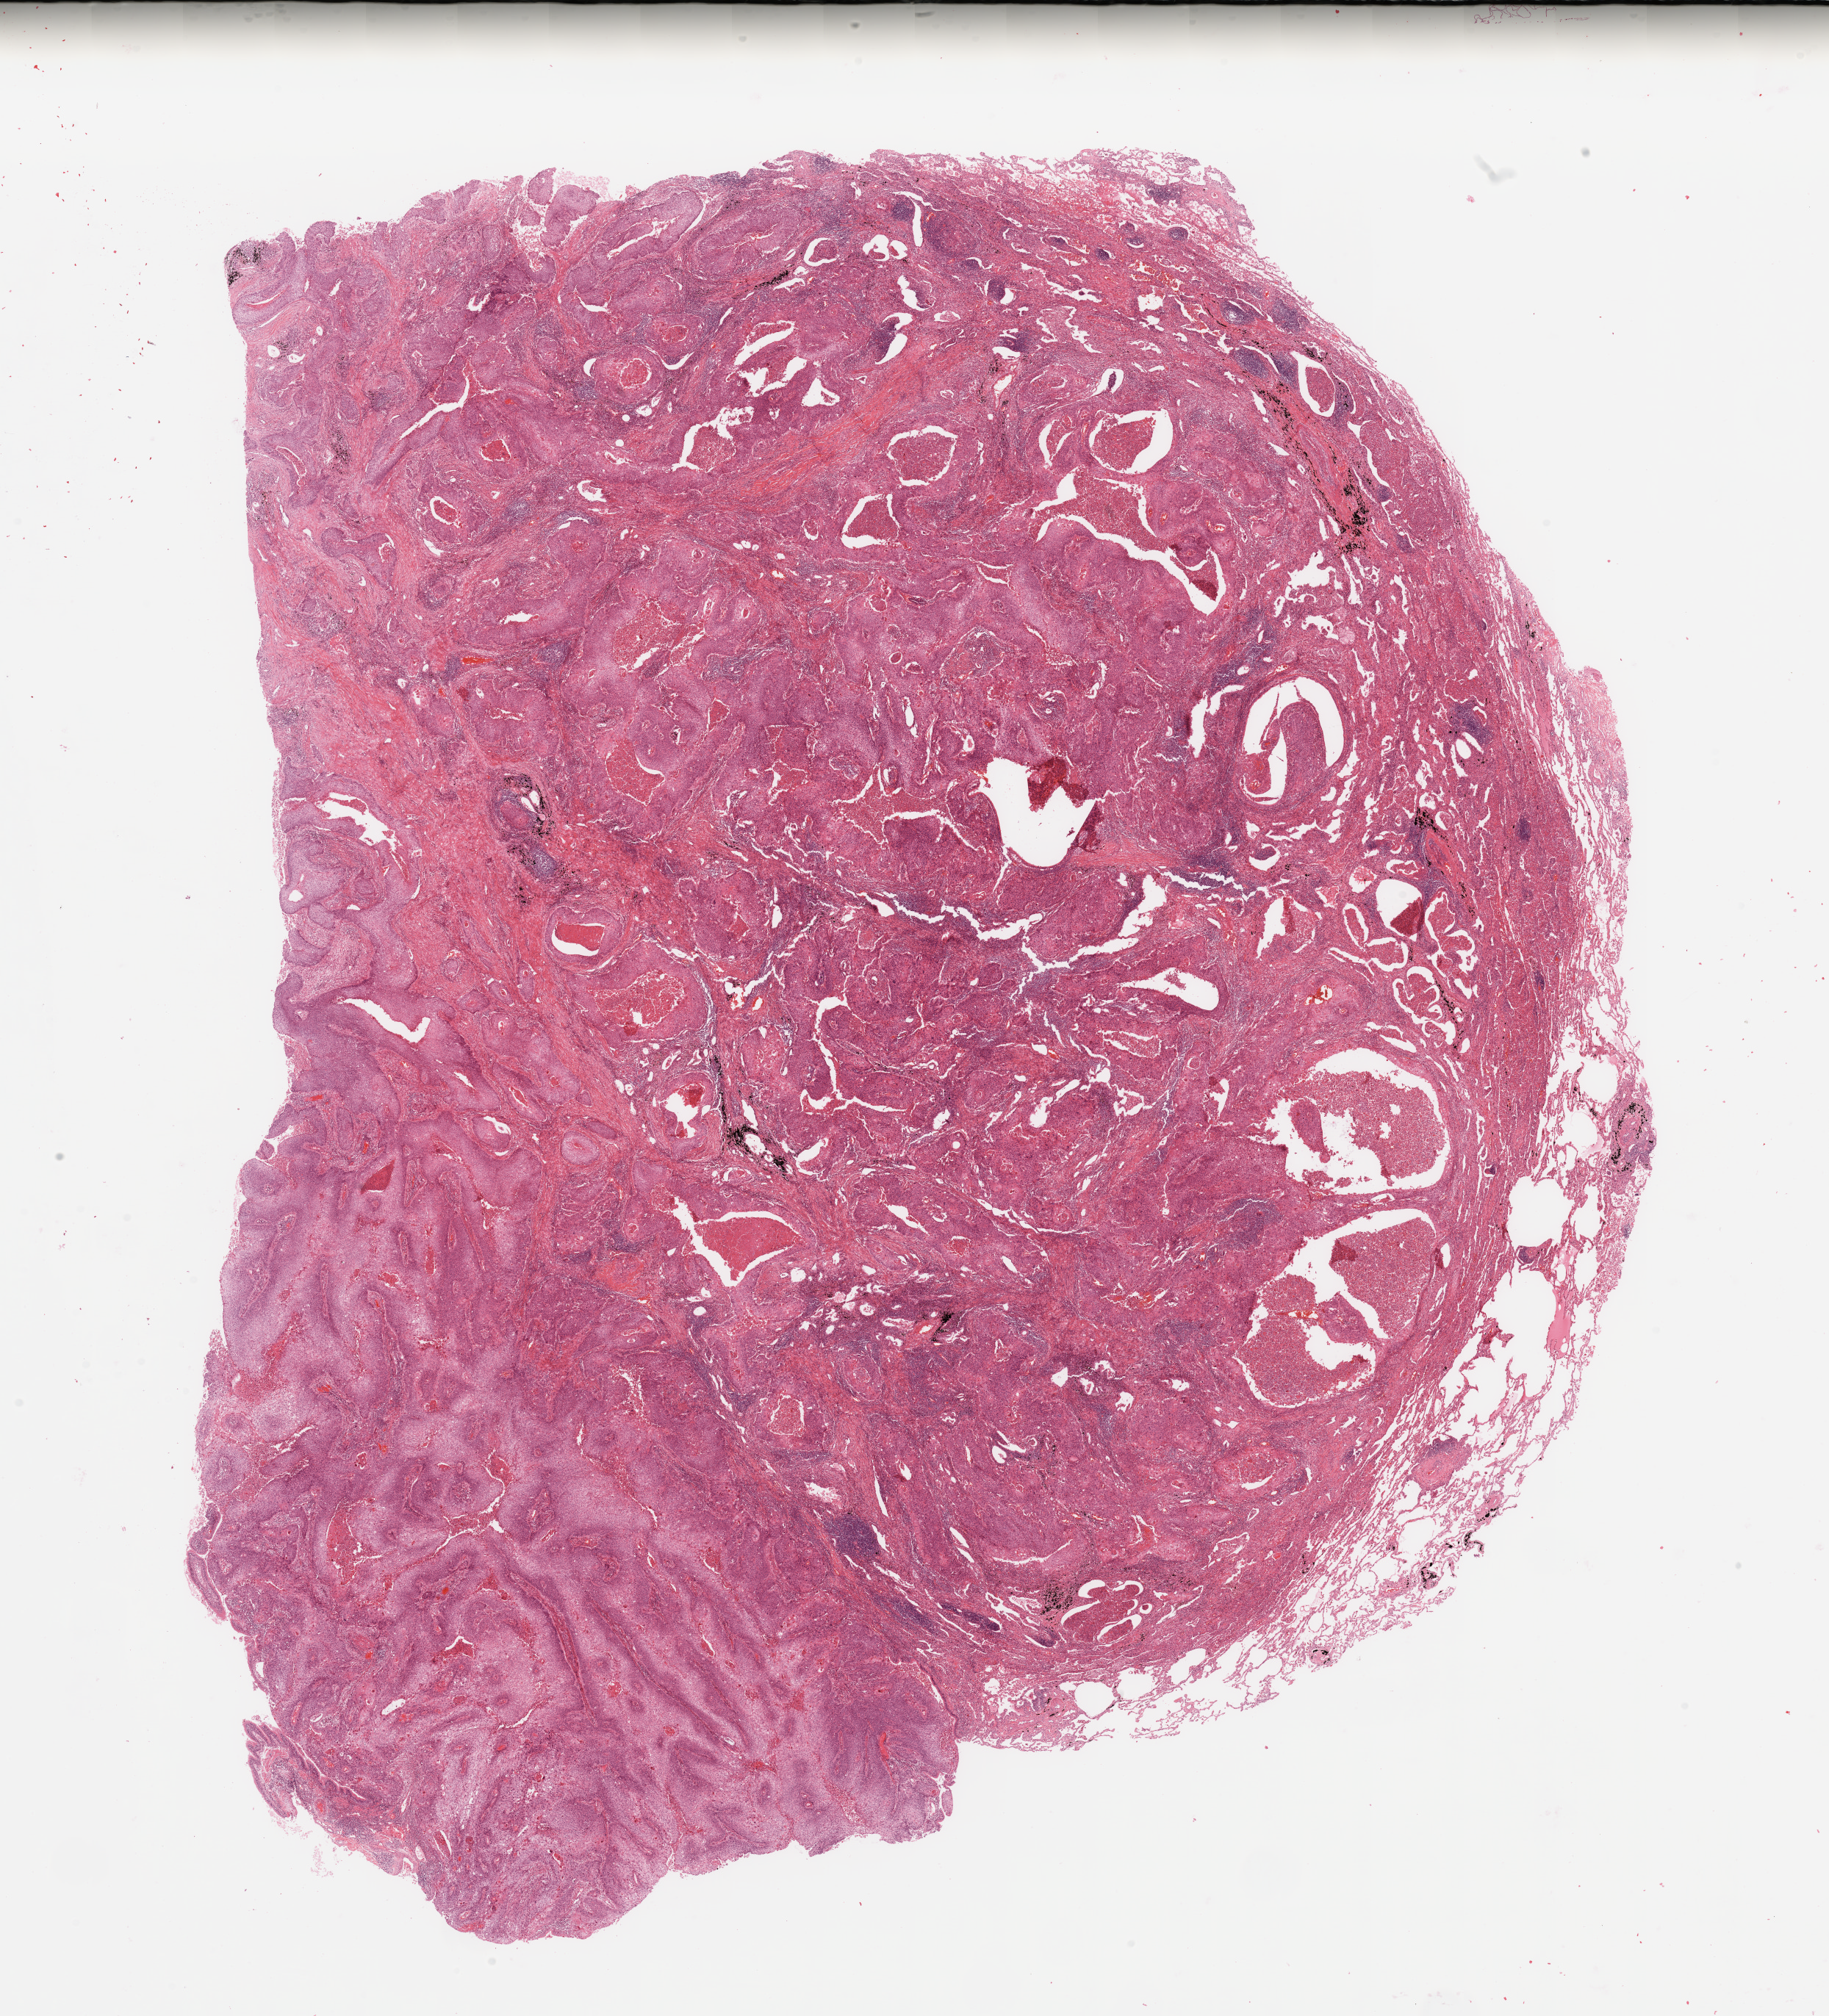
H&E whole-slide image, whole scanned area (about 19.7 x 21.7 mm) shown as a low-resolution overview; tumour tissue sample, lung. 64-year-old male patient. Histologic grade: G3 (poorly differentiated).
* AJCC pathologic stage: IB
* diagnosis: Squamous cell carcinoma, NOS